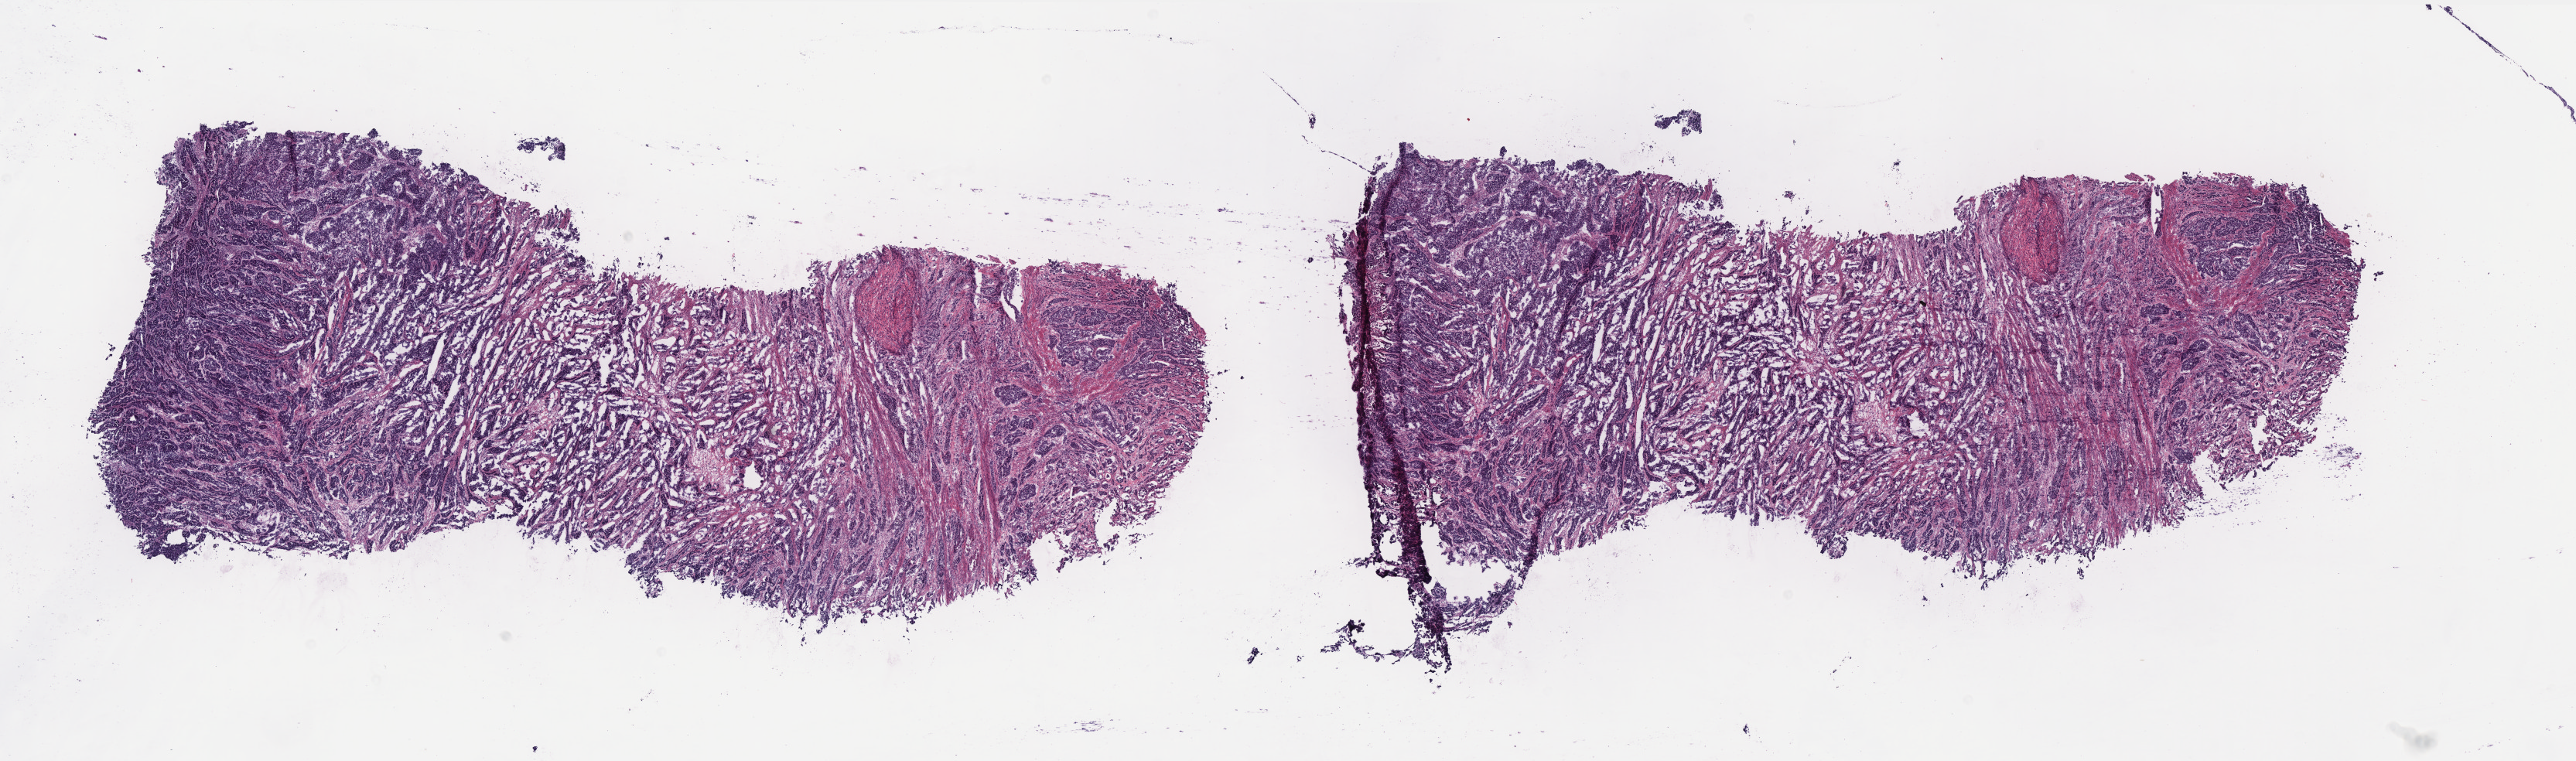
Digitized H&E tissue section (whole slide) — a low-resolution overview of the entire scanned area, about 26.7 x 7.9 mm. Frozen section from the top of the tissue portion. Sample: primary tumour, uterus. Female, age 70 years at initial diagnosis. Histologic grade: G3 (poorly differentiated). Pathologist review of this section (percent, as recorded): tumour cells 60%, tumour nuclei 70%, normal cells 30%, stromal cells 0%, necrosis 10%. Infiltration values recorded for this section: lymphocyte infiltration 10%, monocyte infiltration 0%, neutrophil infiltration 10%.
FIGO stage: IIIC2. Histologic diagnosis: Serous cystadenocarcinoma, NOS (endometrium).